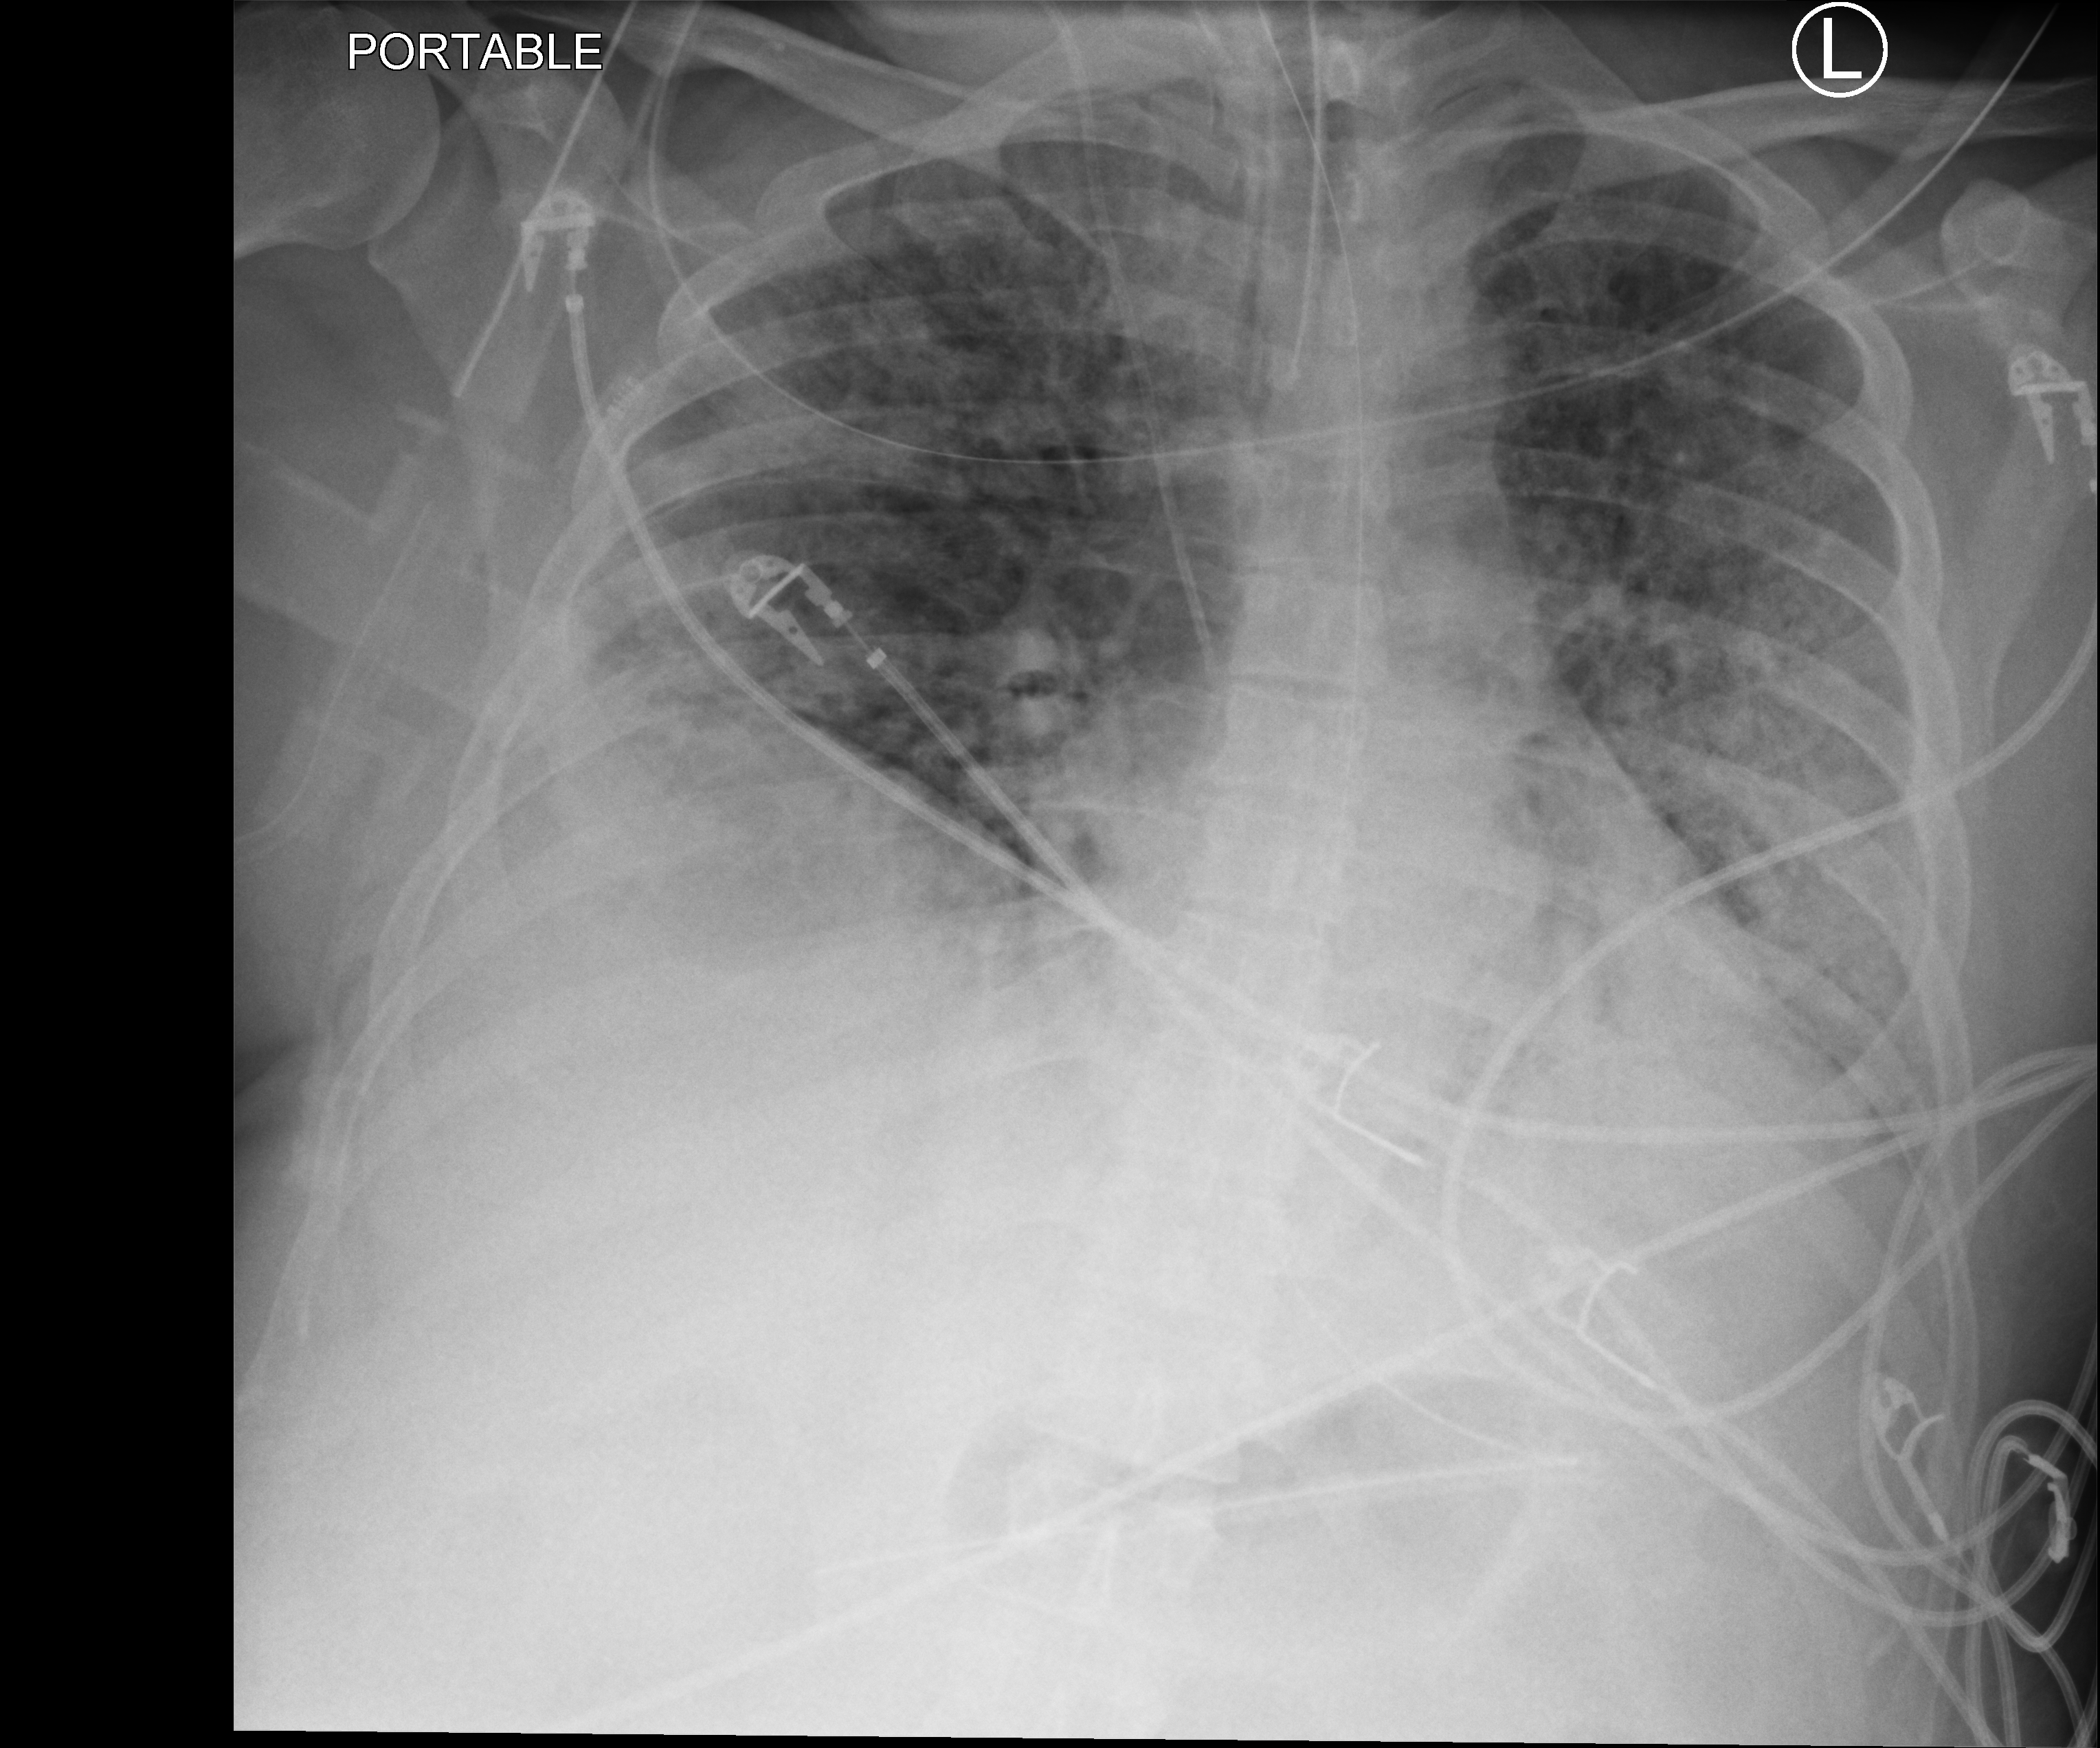
Bedside chest radiograph (computed radiography), anteroposterior (AP) projection. Male patient hospitalised with COVID-19, age 18–59 years.
From the hospital-stay record, not from the radiograph (when in the stay this image was taken is not recorded): length of hospital stay: 96 days; COPD (admission record): no.